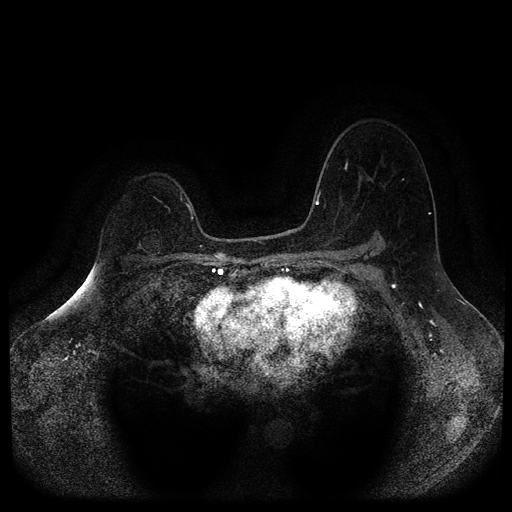
Breast MRI (dynamic contrast-enhanced, multi-phase), one axial slice. Slice 73 of 116 in the series (ordered by position). Dynamic contrast-enhanced series, time point 2 of 5 at this slice position (early post-contrast). 1.5 T. TE 2.6 ms, TR 5.4 ms. 2 mm slice thickness. 512 × 512 image matrix, field of view 340 × 340 mm. Patient: female, 64 years.
Outlined on this slice (semi-automatic segmentation, software-assisted and operator-edited):
- breast lesion (labelled benign in the annotation): box from (x=137, y=231) to (x=162, y=259) px